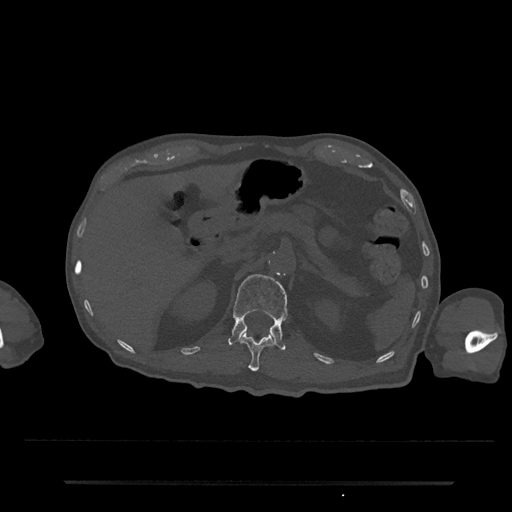
CT including the spine, one axial slice; 120 kVp; bone window (W 1800 / L 400 HU); 0.5 mm slice thickness; 512 × 512 image matrix. Patient: male, 74 years. Case-level facts recorded for this patient, not image findings: primary cancer: prostate.
Outlined on this slice (semi-automatic segmentation, software-assisted and operator-edited):
- L1 vertebra: bounding box (x1, y1, x2, y2) in pixels: (228, 274, 288, 350)
- T12 vertebra: (240, 333, 273, 372)